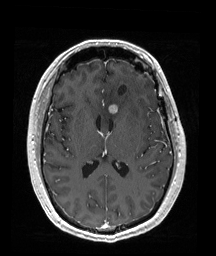
Brain MRI from a brain-tumour surgery series, one axial slice; position 90 of 192 along the scan axis; T1-weighted post-contrast; 1 mm slice thickness; 216 × 256 image matrix. Case-level facts recorded for this patient, not image findings: histopathology: Oligodendroglioma; WHO grade: 2; IDH mutation: yes.
Annotated regions visible in this slice (expert manual segmentation):
- tumour: bounding box (x1, y1, x2, y2) in pixels: (116, 104, 126, 114)